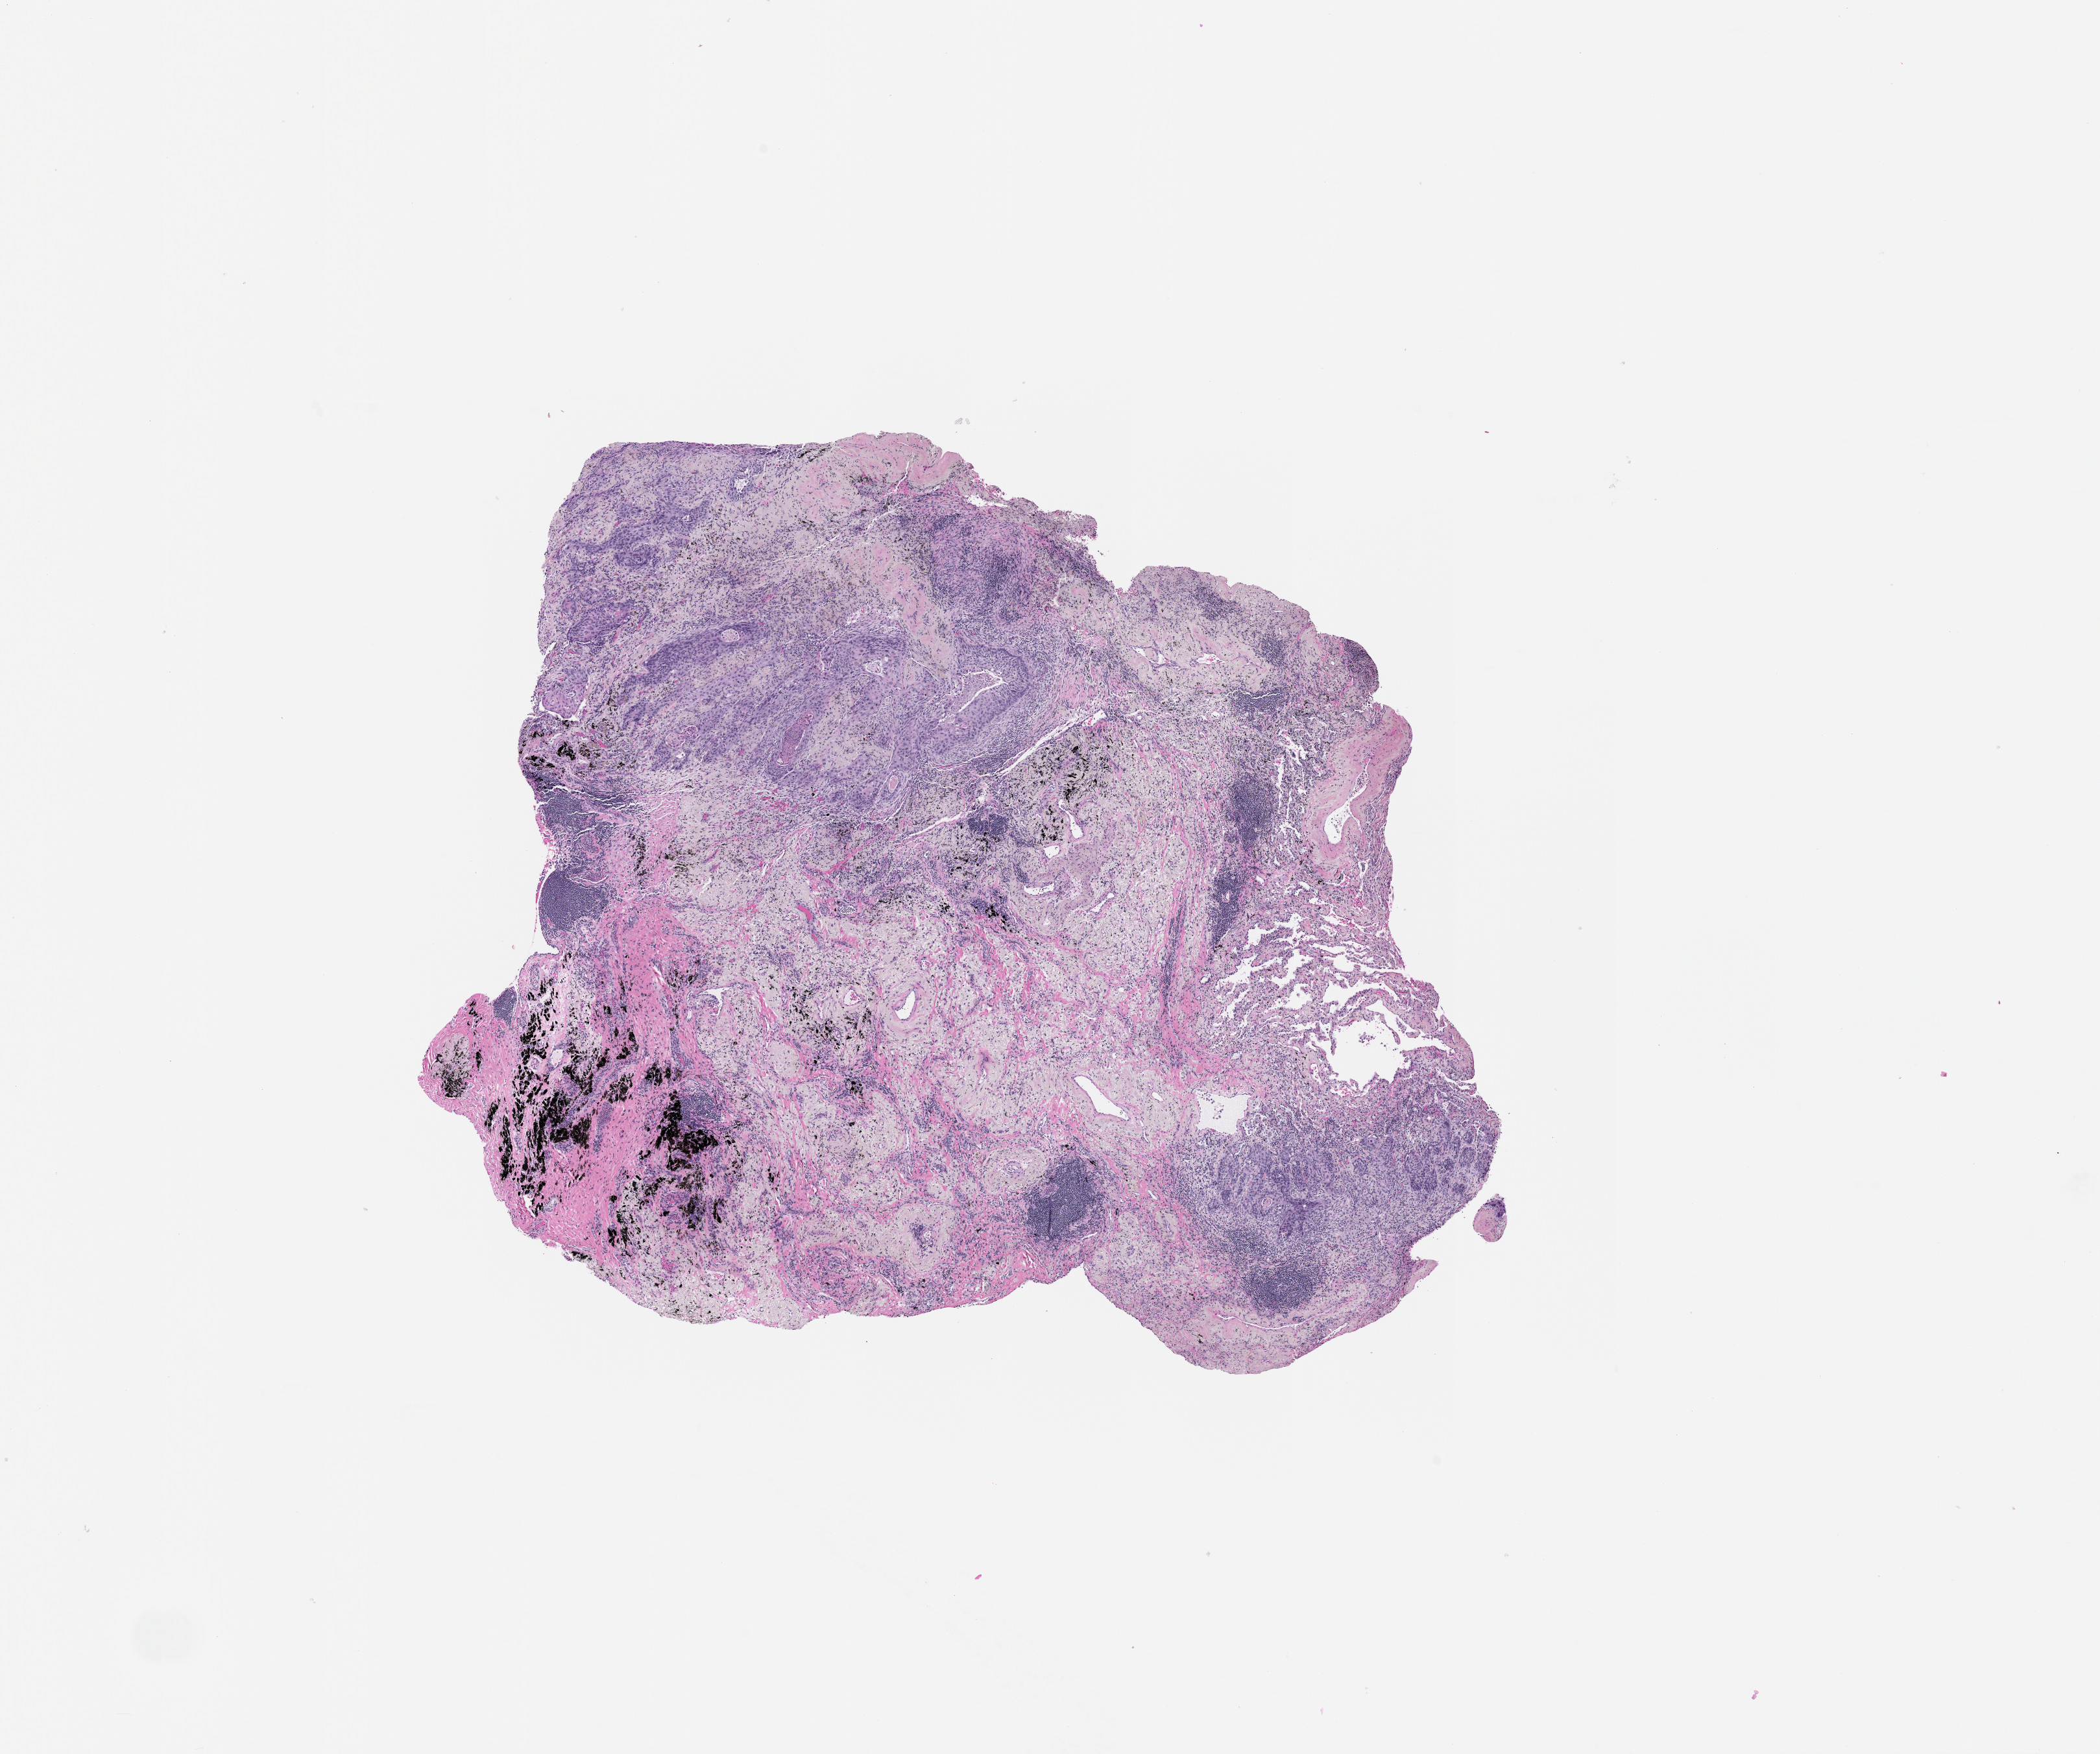
Whole-slide histology image, H&E-stained, whole scanned area (about 13.0 x 10.9 mm) shown as a low-resolution overview; lung, tumour tissue. Female patient.
Patient diagnosis (cohort enrolment): squamous cell carcinoma (lung).